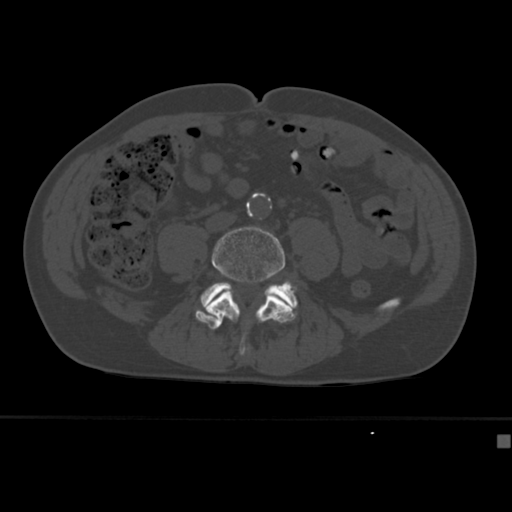
CT including the spine, one axial slice; slice 100 of 430 in the series (ordered by position); reconstruction kernel Br40s; 120 kVp; bone window (W 1800 / L 400 HU); 512 × 512 image matrix. Patient: male, 64 years. From the clinical record (not read from this slice): primary cancer: uterus; vertebrae with lytic lesions (as recorded): T1, T4, T5, T7, L5.
Outlined on this slice (semi-automatically segmented with operator editing):
- L4 vertebra: box from (x=205, y=226) to (x=291, y=356) px
- L5 vertebra: (x=200, y=280)–(x=298, y=331)